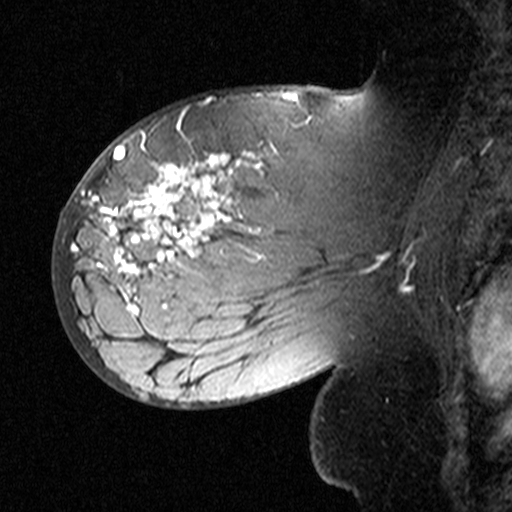
Breast MRI (dynamic contrast-enhanced), one sagittal slice. Position 24 of 44 along the scan axis. Dynamic contrast-enhanced study with each time point stored as its own series, time point 2 of 3 at this slice position (early post-contrast, ordered by acquisition time). 1.5 T. TE 4.5 ms, TR 11 ms. 3 mm slice thickness. 512 × 512 image matrix. Patient: female, 53 years. From the clinical record (not read from this slice): setting: breast cancer imaged before/during neoadjuvant chemotherapy; receptor status: HR-positive, HER2-negative.
Annotated regions visible in this slice (semi-automatically segmented with operator editing):
- analysis volume of interest (the breast-tissue region the enhancement analysis was run in; not a lesion): bounding box [x1, y1, x2, y2] px = [76, 140, 311, 353]
- tumour enhancement mask (voxels above the 90 % enhancement threshold inside the analysis volume of interest): [97, 151, 262, 316]